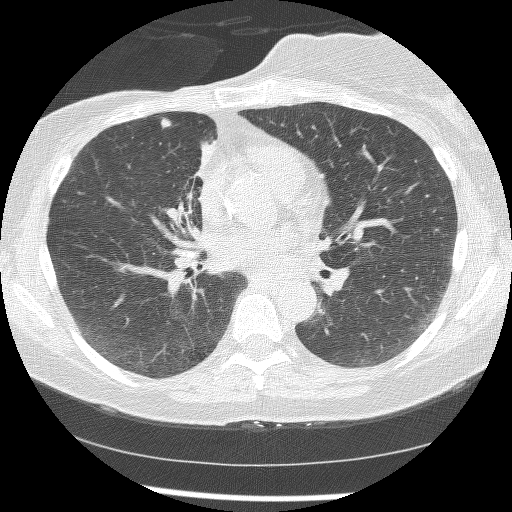
Low-dose screening chest CT, axial slice. Baseline screening round. Lung window (W 1500 / L -600 HU). Lung (sharp) reconstruction kernel (BONE). Slice 76 of 172 in the series. Female participant, aged 56 years at enrolment. Current smoker at enrolment.
Lesion marked by an expert reader, bounding box [x1, y1, x2, y2] px = [150, 111, 179, 141]. The screening reader recorded 2 non-calcified nodules or masses ≥4 mm on this exam (right lower lobe, right middle lobe); which of them this box marks is not recorded. Later outcome: lung cancer diagnosed 1185 days after this screen — adenocarcinoma, NOS, right upper lobe, stage IIIB (AJCC 6th edition), 8 mm at pathology.